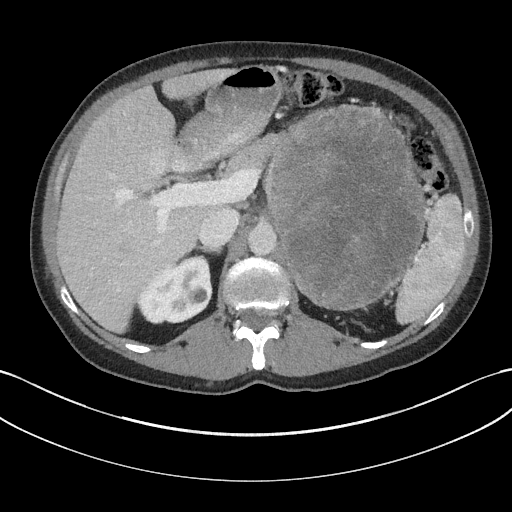
Contrast-enhanced abdominal CT, one axial slice. 100 kVp. Intravenous contrast given. Soft-tissue window (W 400 / L 40 HU). 3 mm slice thickness. 512 × 512 image matrix, field of view 384 × 384 mm. Patient: male, 58 years. Case-level facts recorded for this patient, not image findings: diagnosis: adrenocortical carcinoma; tumour side: left adrenal; tumour size at pathology: 22 cm; Ki-67 index: 26 %; stage (as recorded): 2.
Outlined on this slice (semi-automatic segmentation, software-assisted and operator-edited):
- mass: box from (x=265, y=107) to (x=423, y=309) px